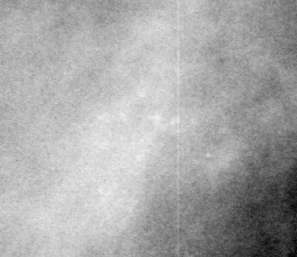
Crop from a digitized film mammogram around one marked abnormality, left breast, CC view, BI-RADS breast density category 3 (scale 1–4).
- Finding: calcifications, morphology amorphous / pleomorphic, distribution clustered; BI-RADS assessment category 4; pathology result (as recorded, not read from the image): malignant.